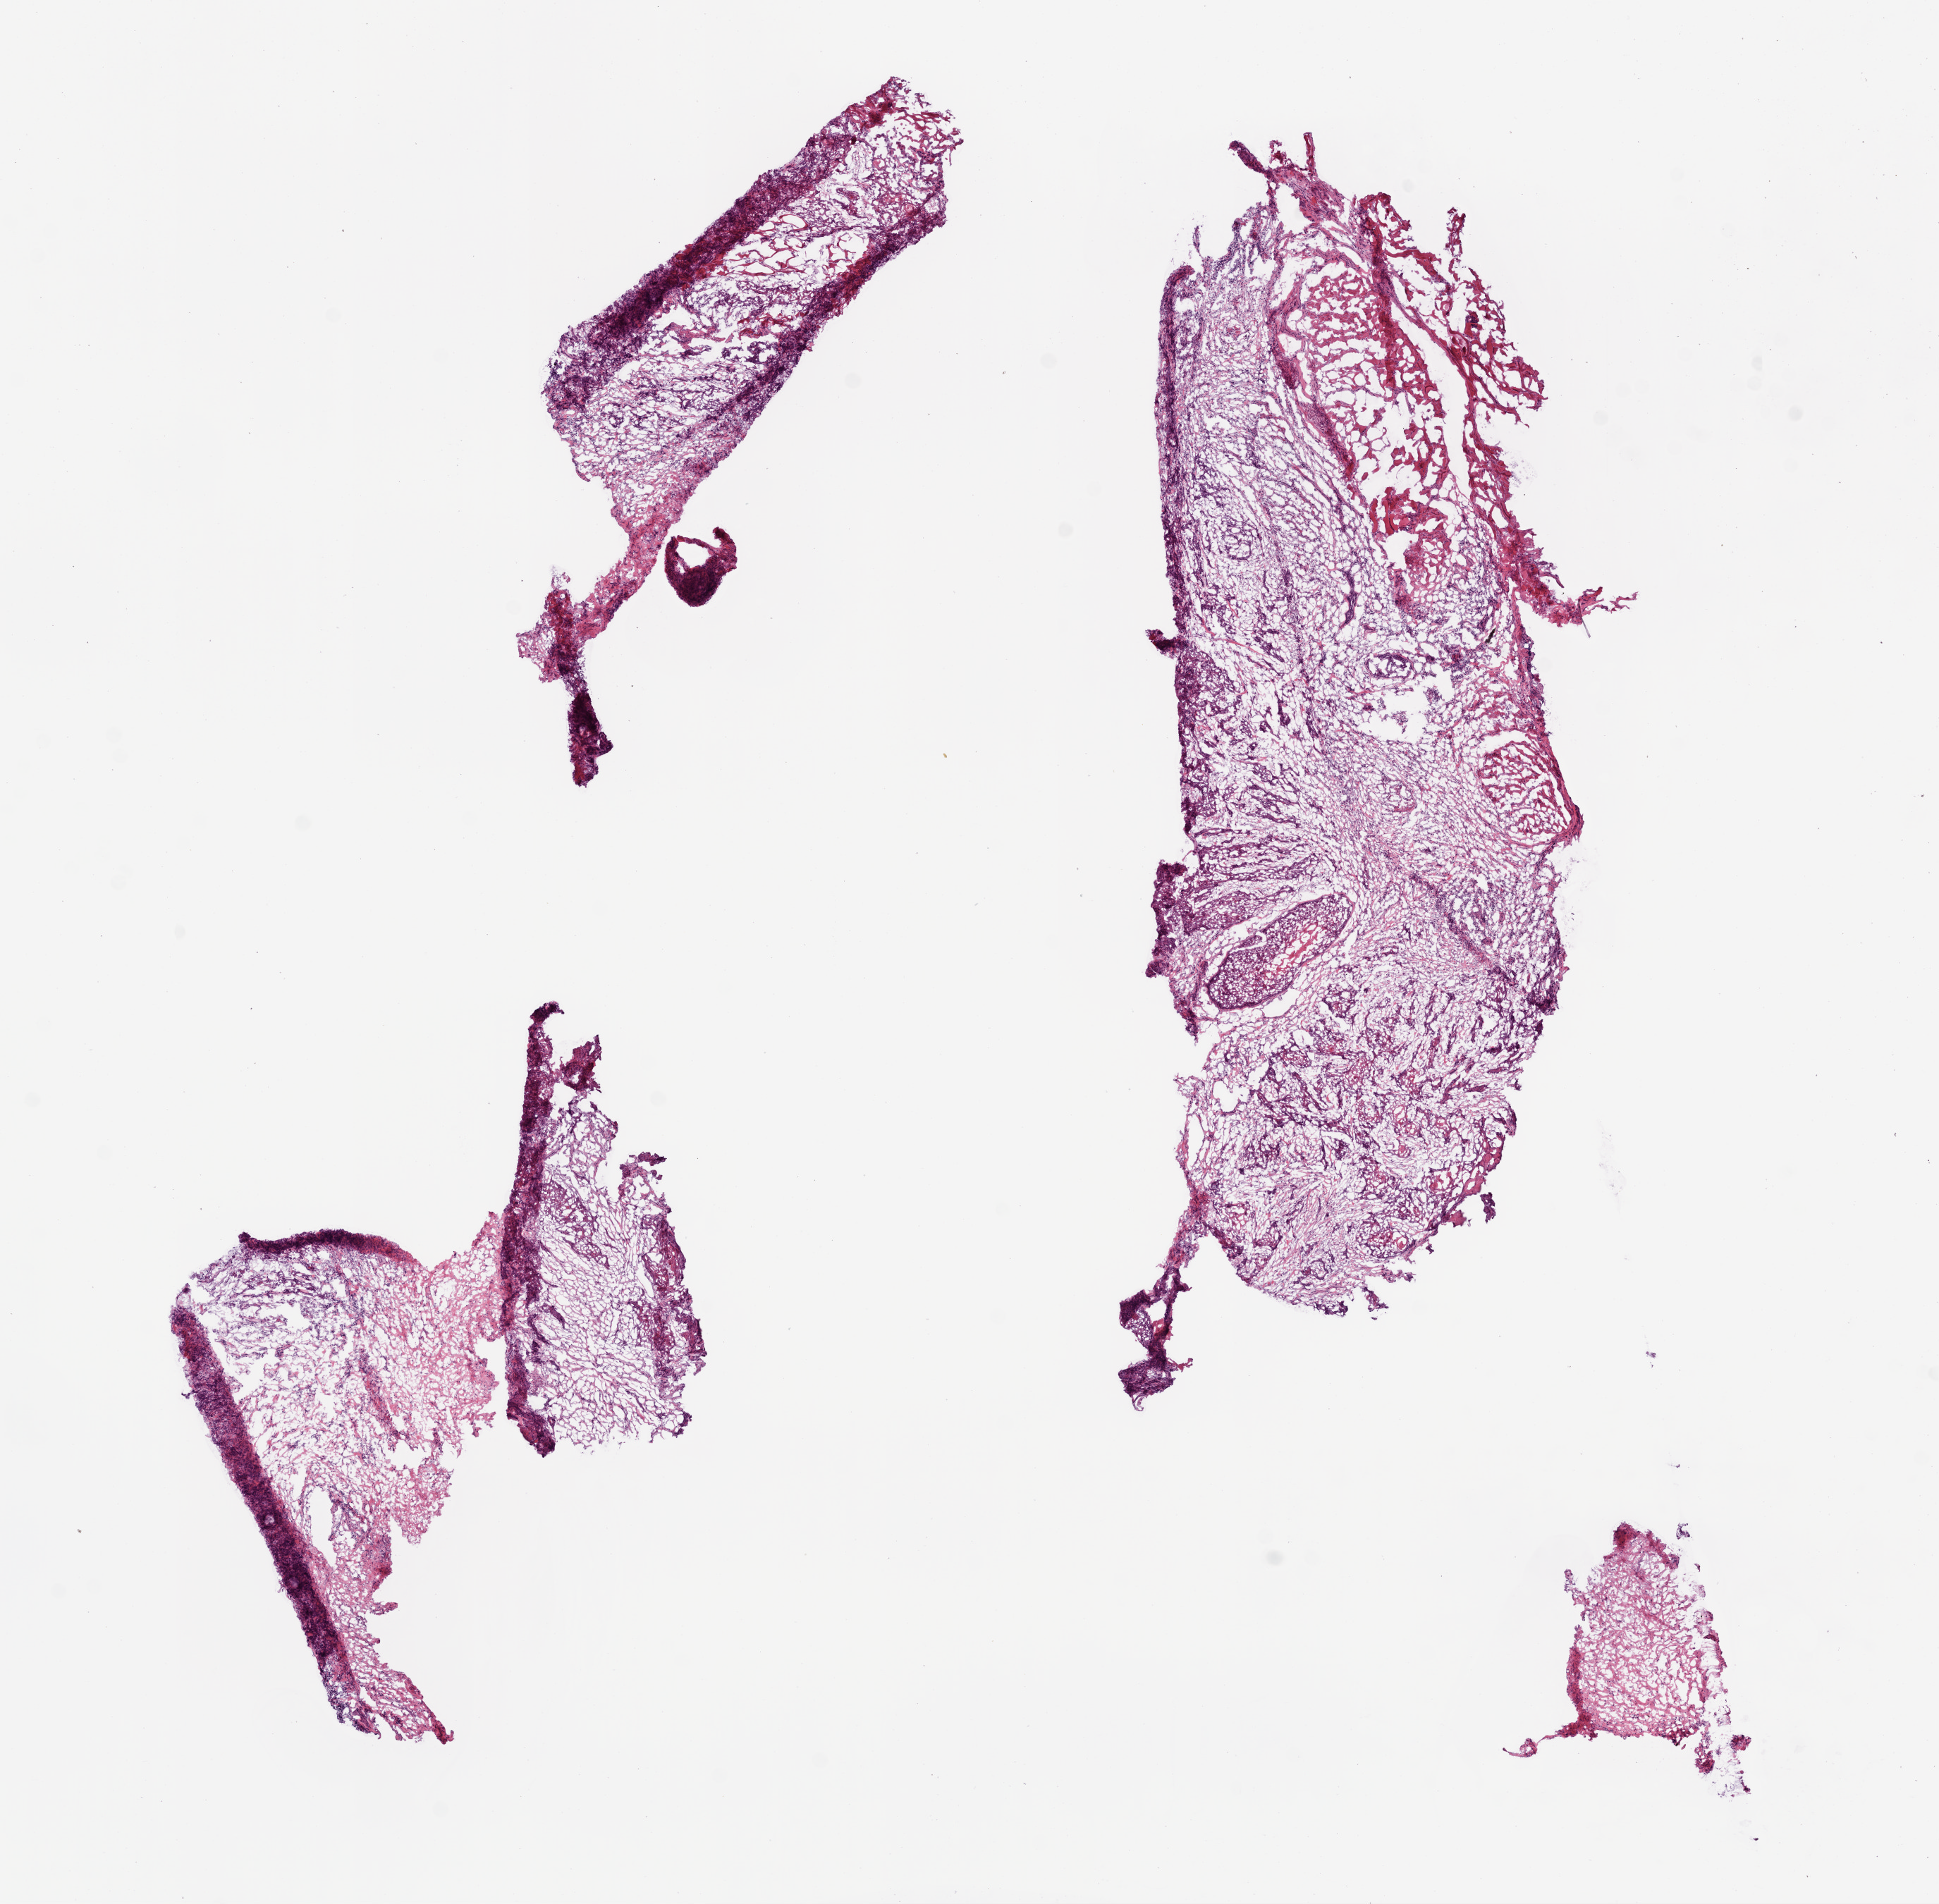
Whole-slide histology image, Hematoxylin and eosin (H&E) stained — shown as a low-resolution overview of the whole scanned area (about 11.0 x 10.8 mm, acquisition: 20x scan). Frozen section from the bottom of the tissue portion. Head and neck, primary tumour sample. Female patient; age at initial diagnosis 60 years. Histologic grade: G2 (moderately differentiated). Composition of this section per pathologist review: tumour cells 75%, tumour nuclei 70%, normal cells 0%, stromal cells 25%, necrosis 0%.
Pathologic diagnosis: Squamous cell carcinoma, NOS (tongue, NOS). TNM: T4a N2b M0. AJCC pathologic stage: IVA (6th edition).